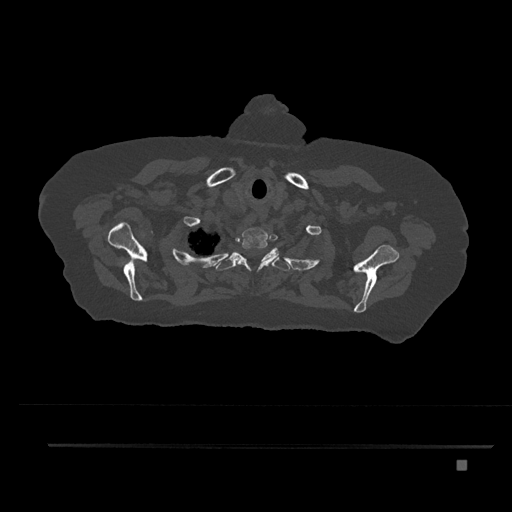
CT including the spine, one axial slice. Slice 684 of 797 in the series (ordered by position). Reconstruction kernel Br40s/3. 120 kVp. Bone window (W 1800 / L 400 HU). 512 × 512 image matrix. Patient: female, 76 years. Case-level facts recorded for this patient, not image findings: primary cancer: lung; vertebrae with lytic lesions (as recorded): T11, L3.
Structures marked on this image (semi-automatic segmentation, software-assisted and operator-edited):
- T1 vertebra: bounding box [x1, y1, x2, y2] px = [236, 227, 279, 271]
- T2 vertebra: [207, 247, 290, 272]